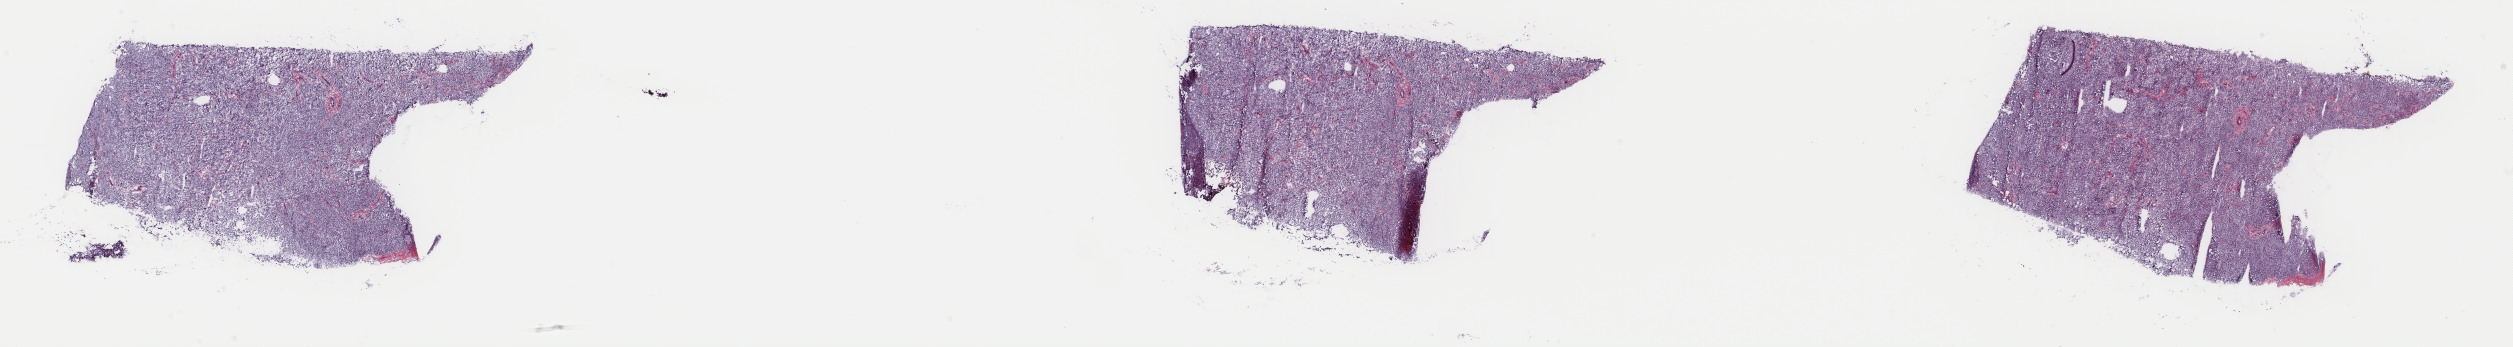
Hematoxylin and eosin (H&E) stained whole-slide image, low-resolution overview of the scanned area, about 39.9 x 5.5 mm (acquisition: 40x scan). Frozen section. Metastatic tumour sample, sampled site not recorded. Patient: male, age at initial diagnosis 56 years. Composition of this section per pathologist review: tumour cells 100%, tumour nuclei 80%, normal cells 0%, stromal cells 0%, necrosis 0%. Infiltration values recorded for this section: lymphocyte infiltration 2%, monocyte infiltration 0%, neutrophil infiltration 0%.
This section: metastatic tumour tissue. Patient diagnosis: Malignant melanoma, NOS.